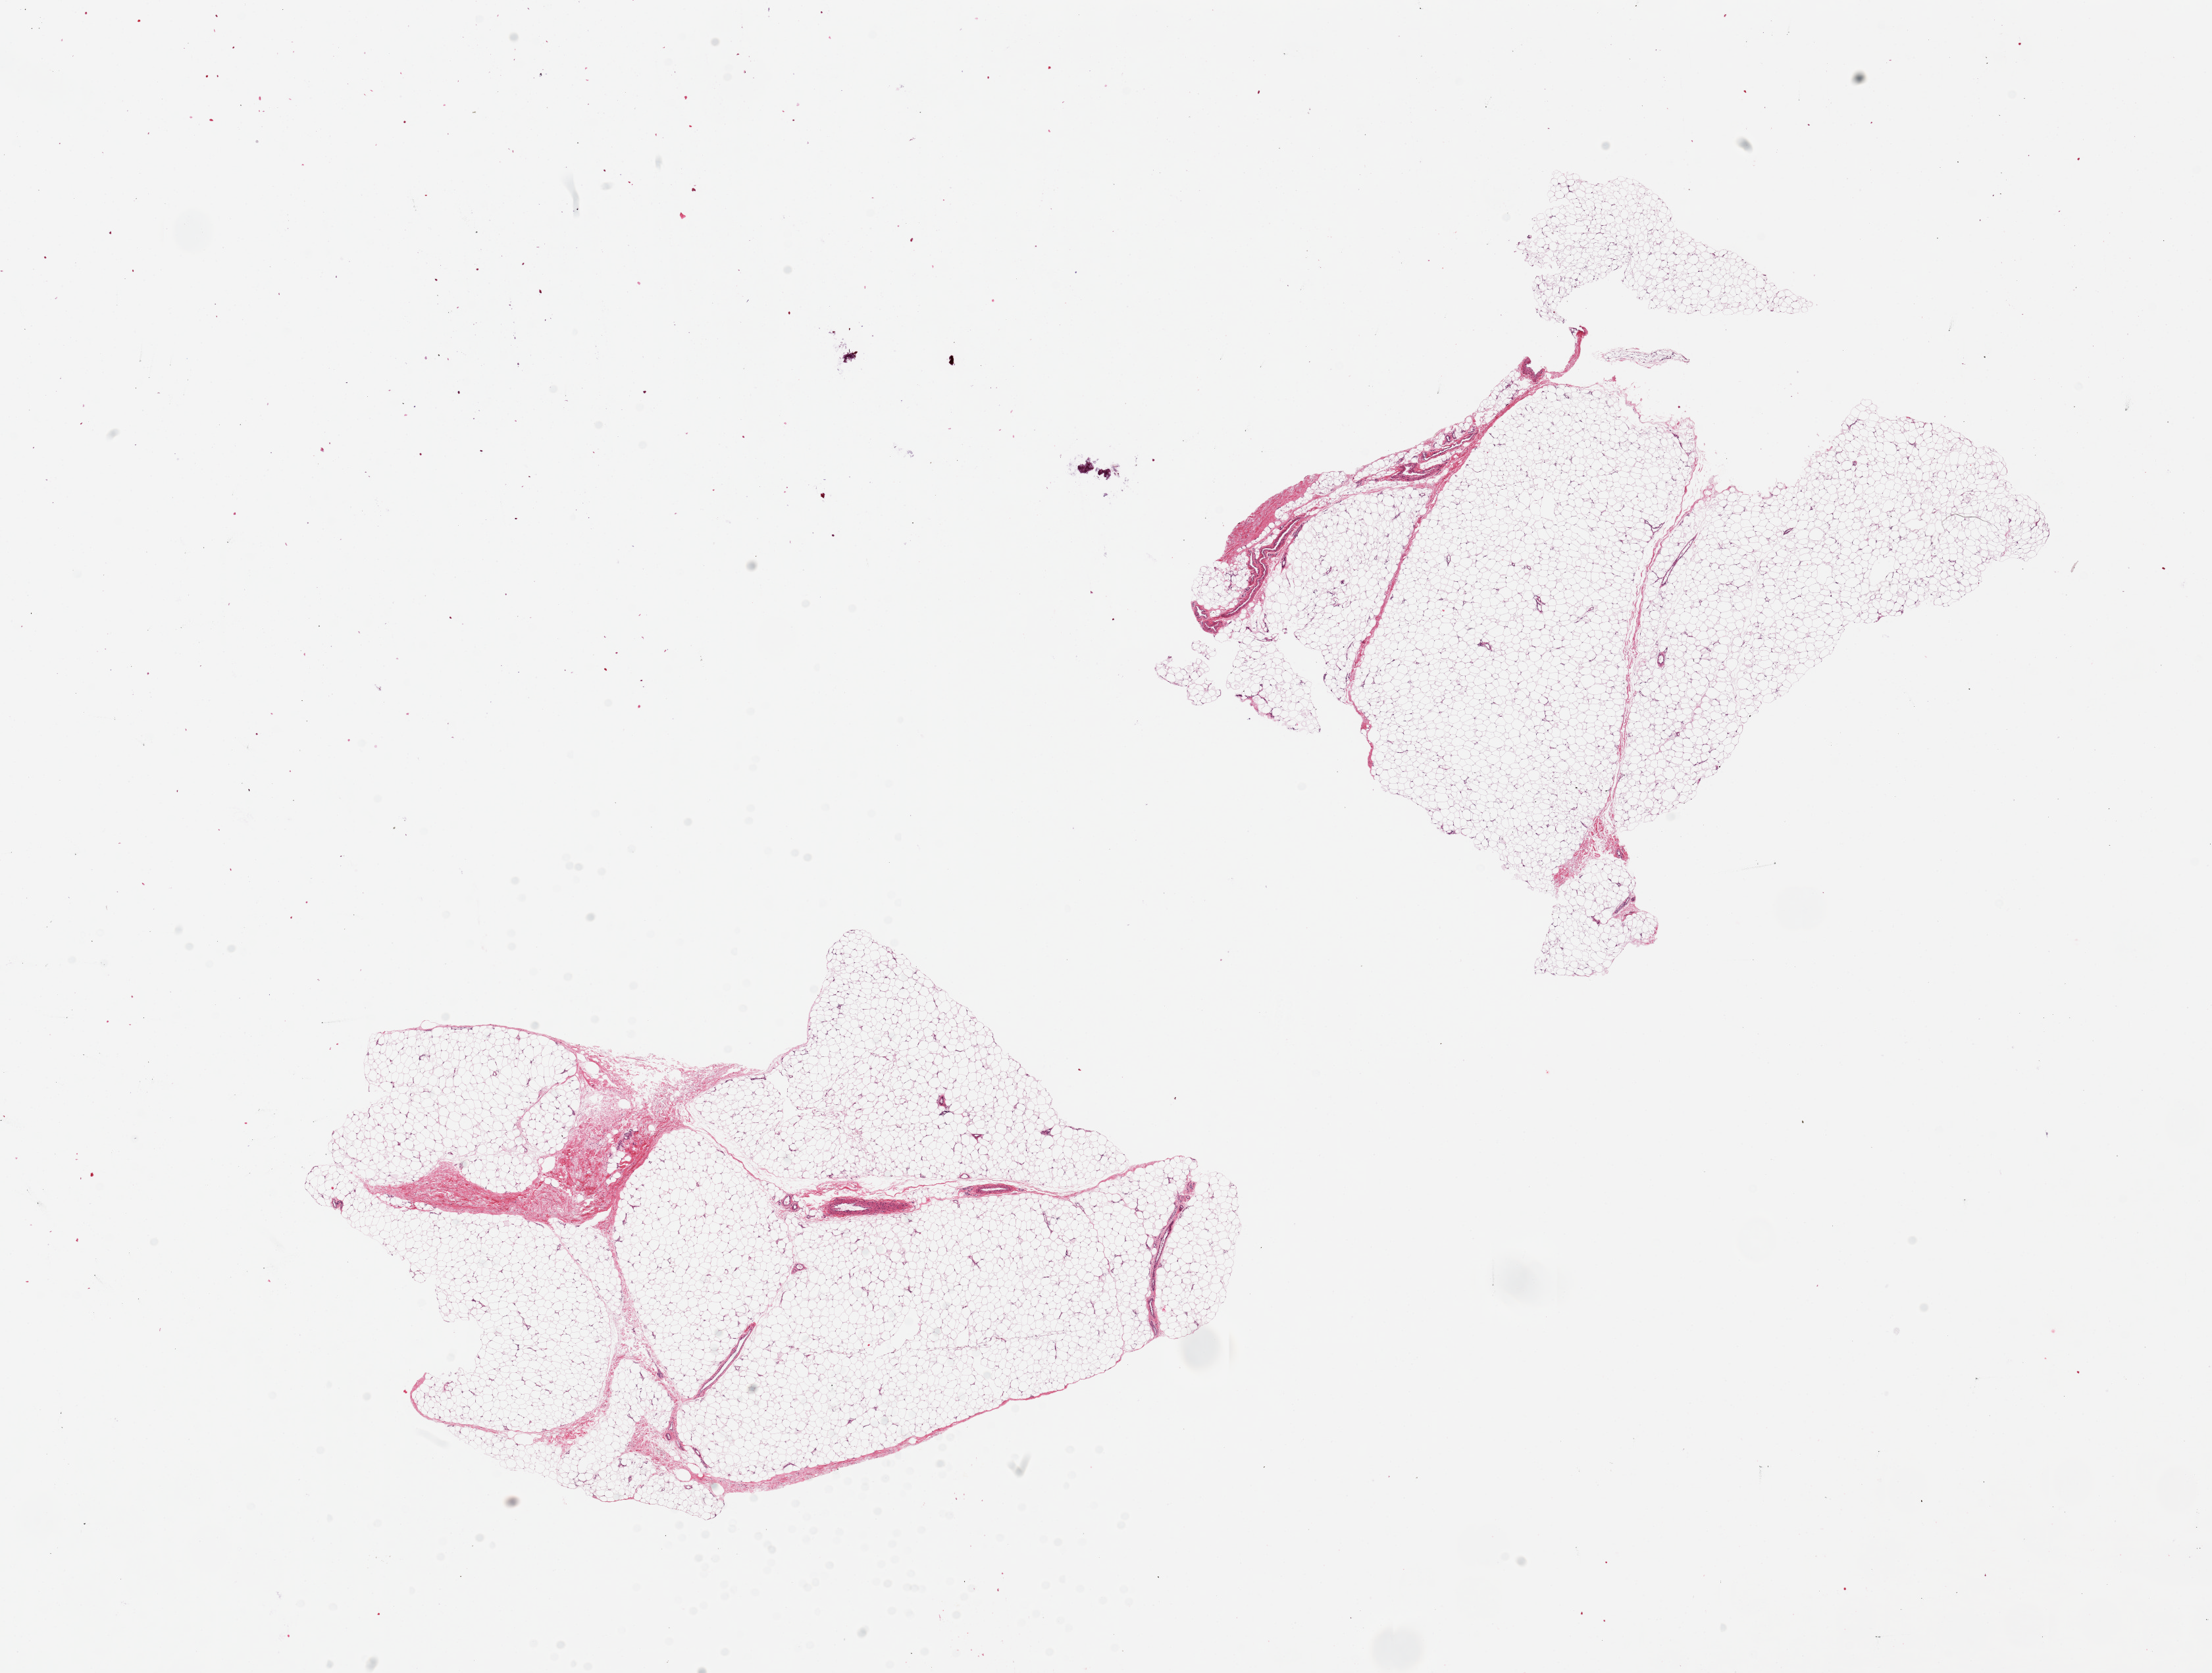
Haematoxylin and eosin whole-slide image, shown as a low-resolution overview of the whole scanned area (about 26.6 x 20.1 mm); PAXgene-fixed, paraffin-embedded tissue; target tissue: adipose tissue; tissue donor sample. Donor: female.
Pathologist's review note for this sample: 2 pieces, 11x7 & 8x7mm; No defects.